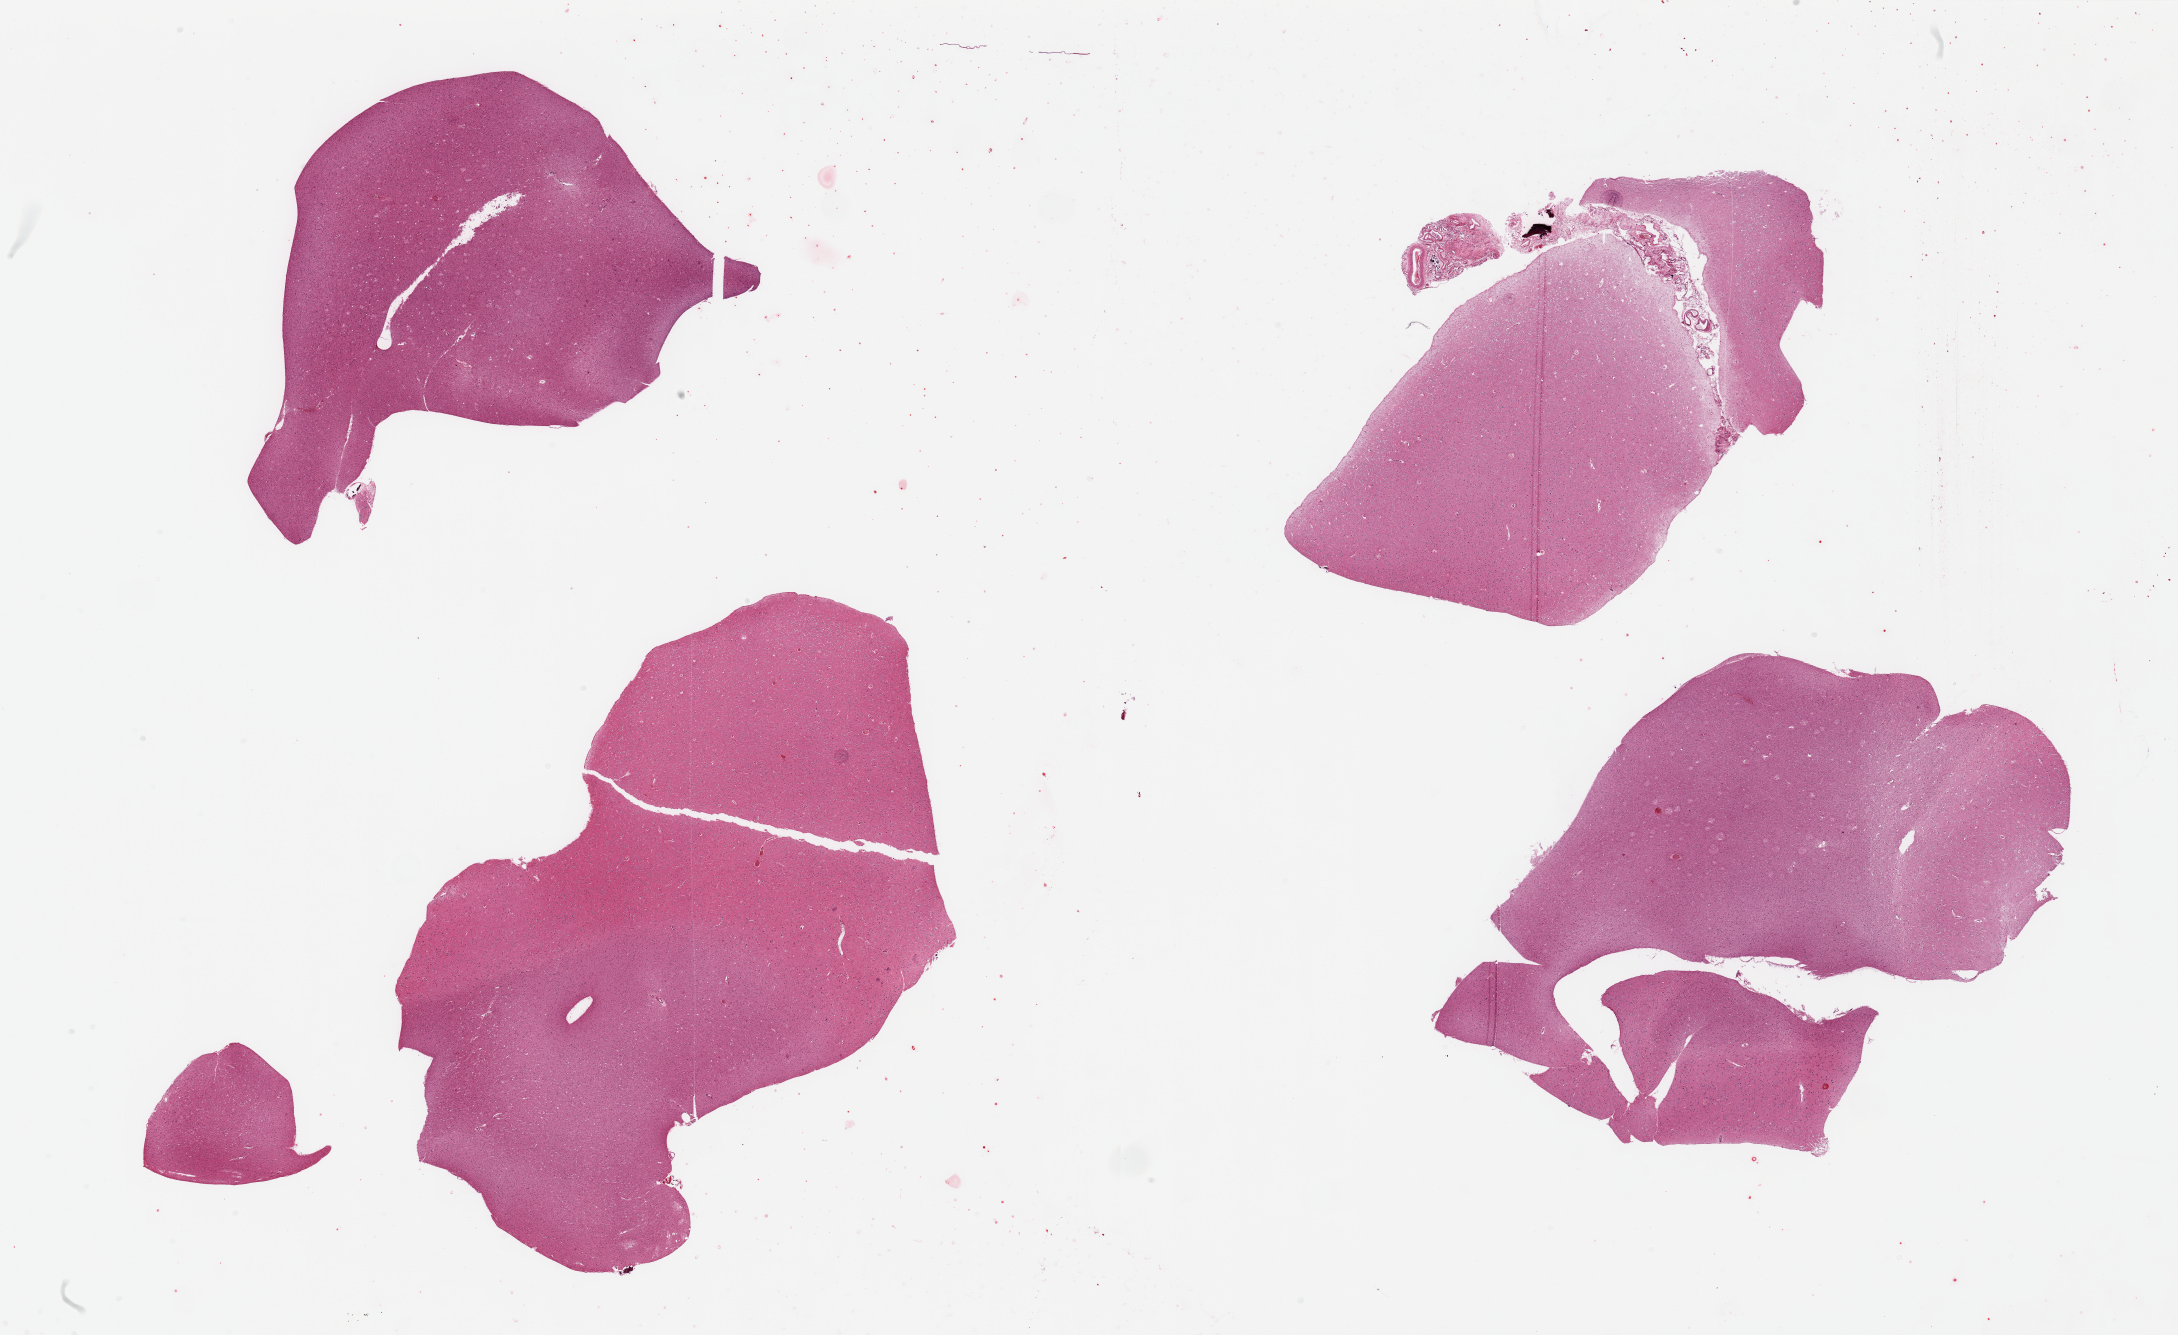
Haematoxylin and eosin whole-slide image, shown as a low-resolution overview of the whole scanned area (about 34.5 x 21.1 mm, slide scanned at 20x). PAXgene-fixed, paraffin-embedded tissue. Sampled site (target tissue): cerebral cortex. Donor tissue sample. Female donor.
Reviewer comment on this tissue sample: 4 pieces (fragmented); some meninges present, includes significant white matter.